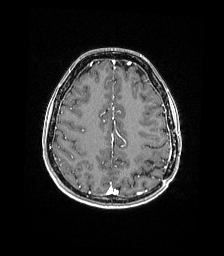
Brain MRI from a brain-tumour surgery series, one axial slice; slice 57 of 176 in the series (ordered by position); T1-weighted post-contrast; 1 mm slice thickness; 224 × 256 image matrix. Case-level facts recorded for this patient, not image findings: histopathology: Atypical meningioma; WHO grade: 2.
Structures marked on this image (expert manual segmentation):
- previous resection cavity: box from (x=150, y=161) to (x=153, y=163) px